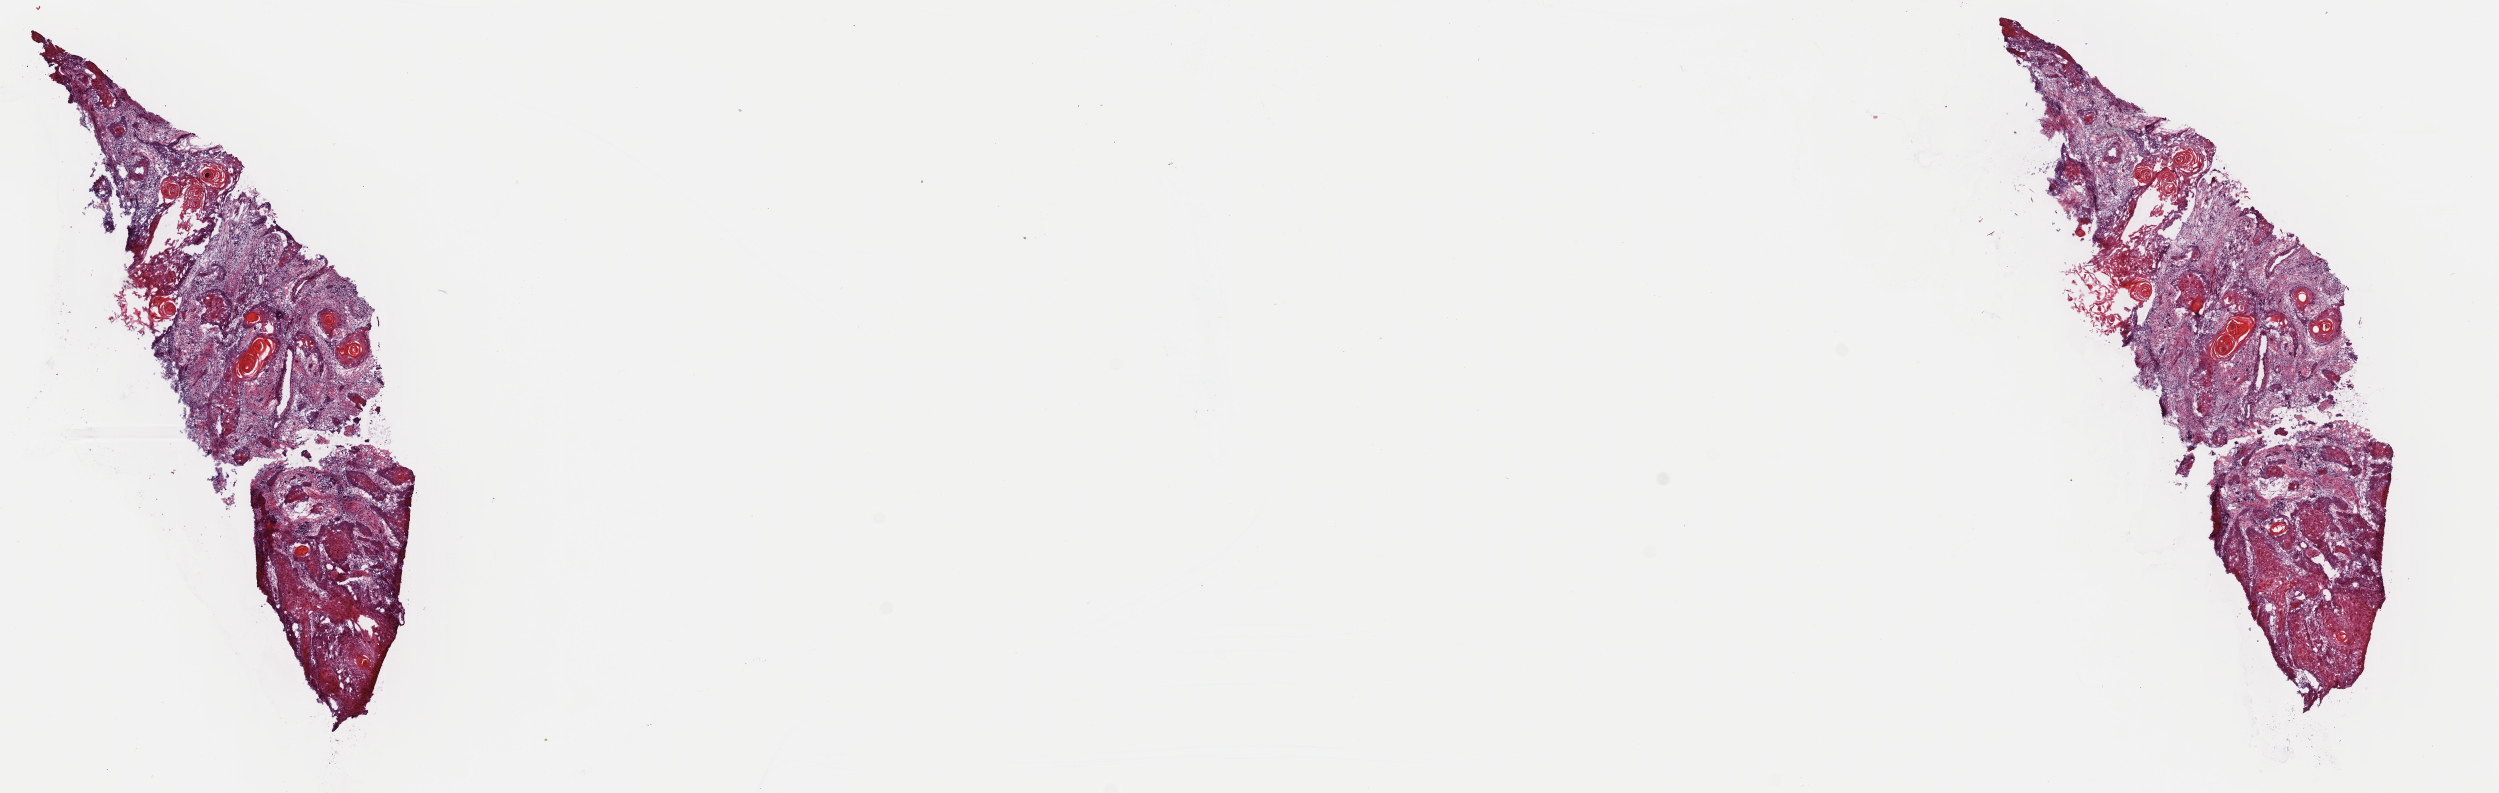
Digitized Hematoxylin and eosin (H&E) stained tissue section (whole slide), a low-resolution overview of the entire scanned area, about 19.7 x 6.3 mm (from a 40x scan). Frozen section. Sample: primary tumour, head and neck. Patient: male, age at initial diagnosis 54 years. Histologic grade: G1 (well differentiated). Pathologist review of this section (percent, as recorded): tumour cells 60%, tumour nuclei 70%, normal cells 10%, stromal cells 30%, necrosis 0%. Infiltration values recorded for this section: lymphocyte infiltration 10%, monocyte infiltration 0%, neutrophil infiltration 0%.
- AJCC pathologic stage: IVA (7th edition)
- lymph nodes positive (case pathology): 2 of 73 examined
- diagnosis: Squamous cell carcinoma, keratinizing, NOS (tongue, NOS)